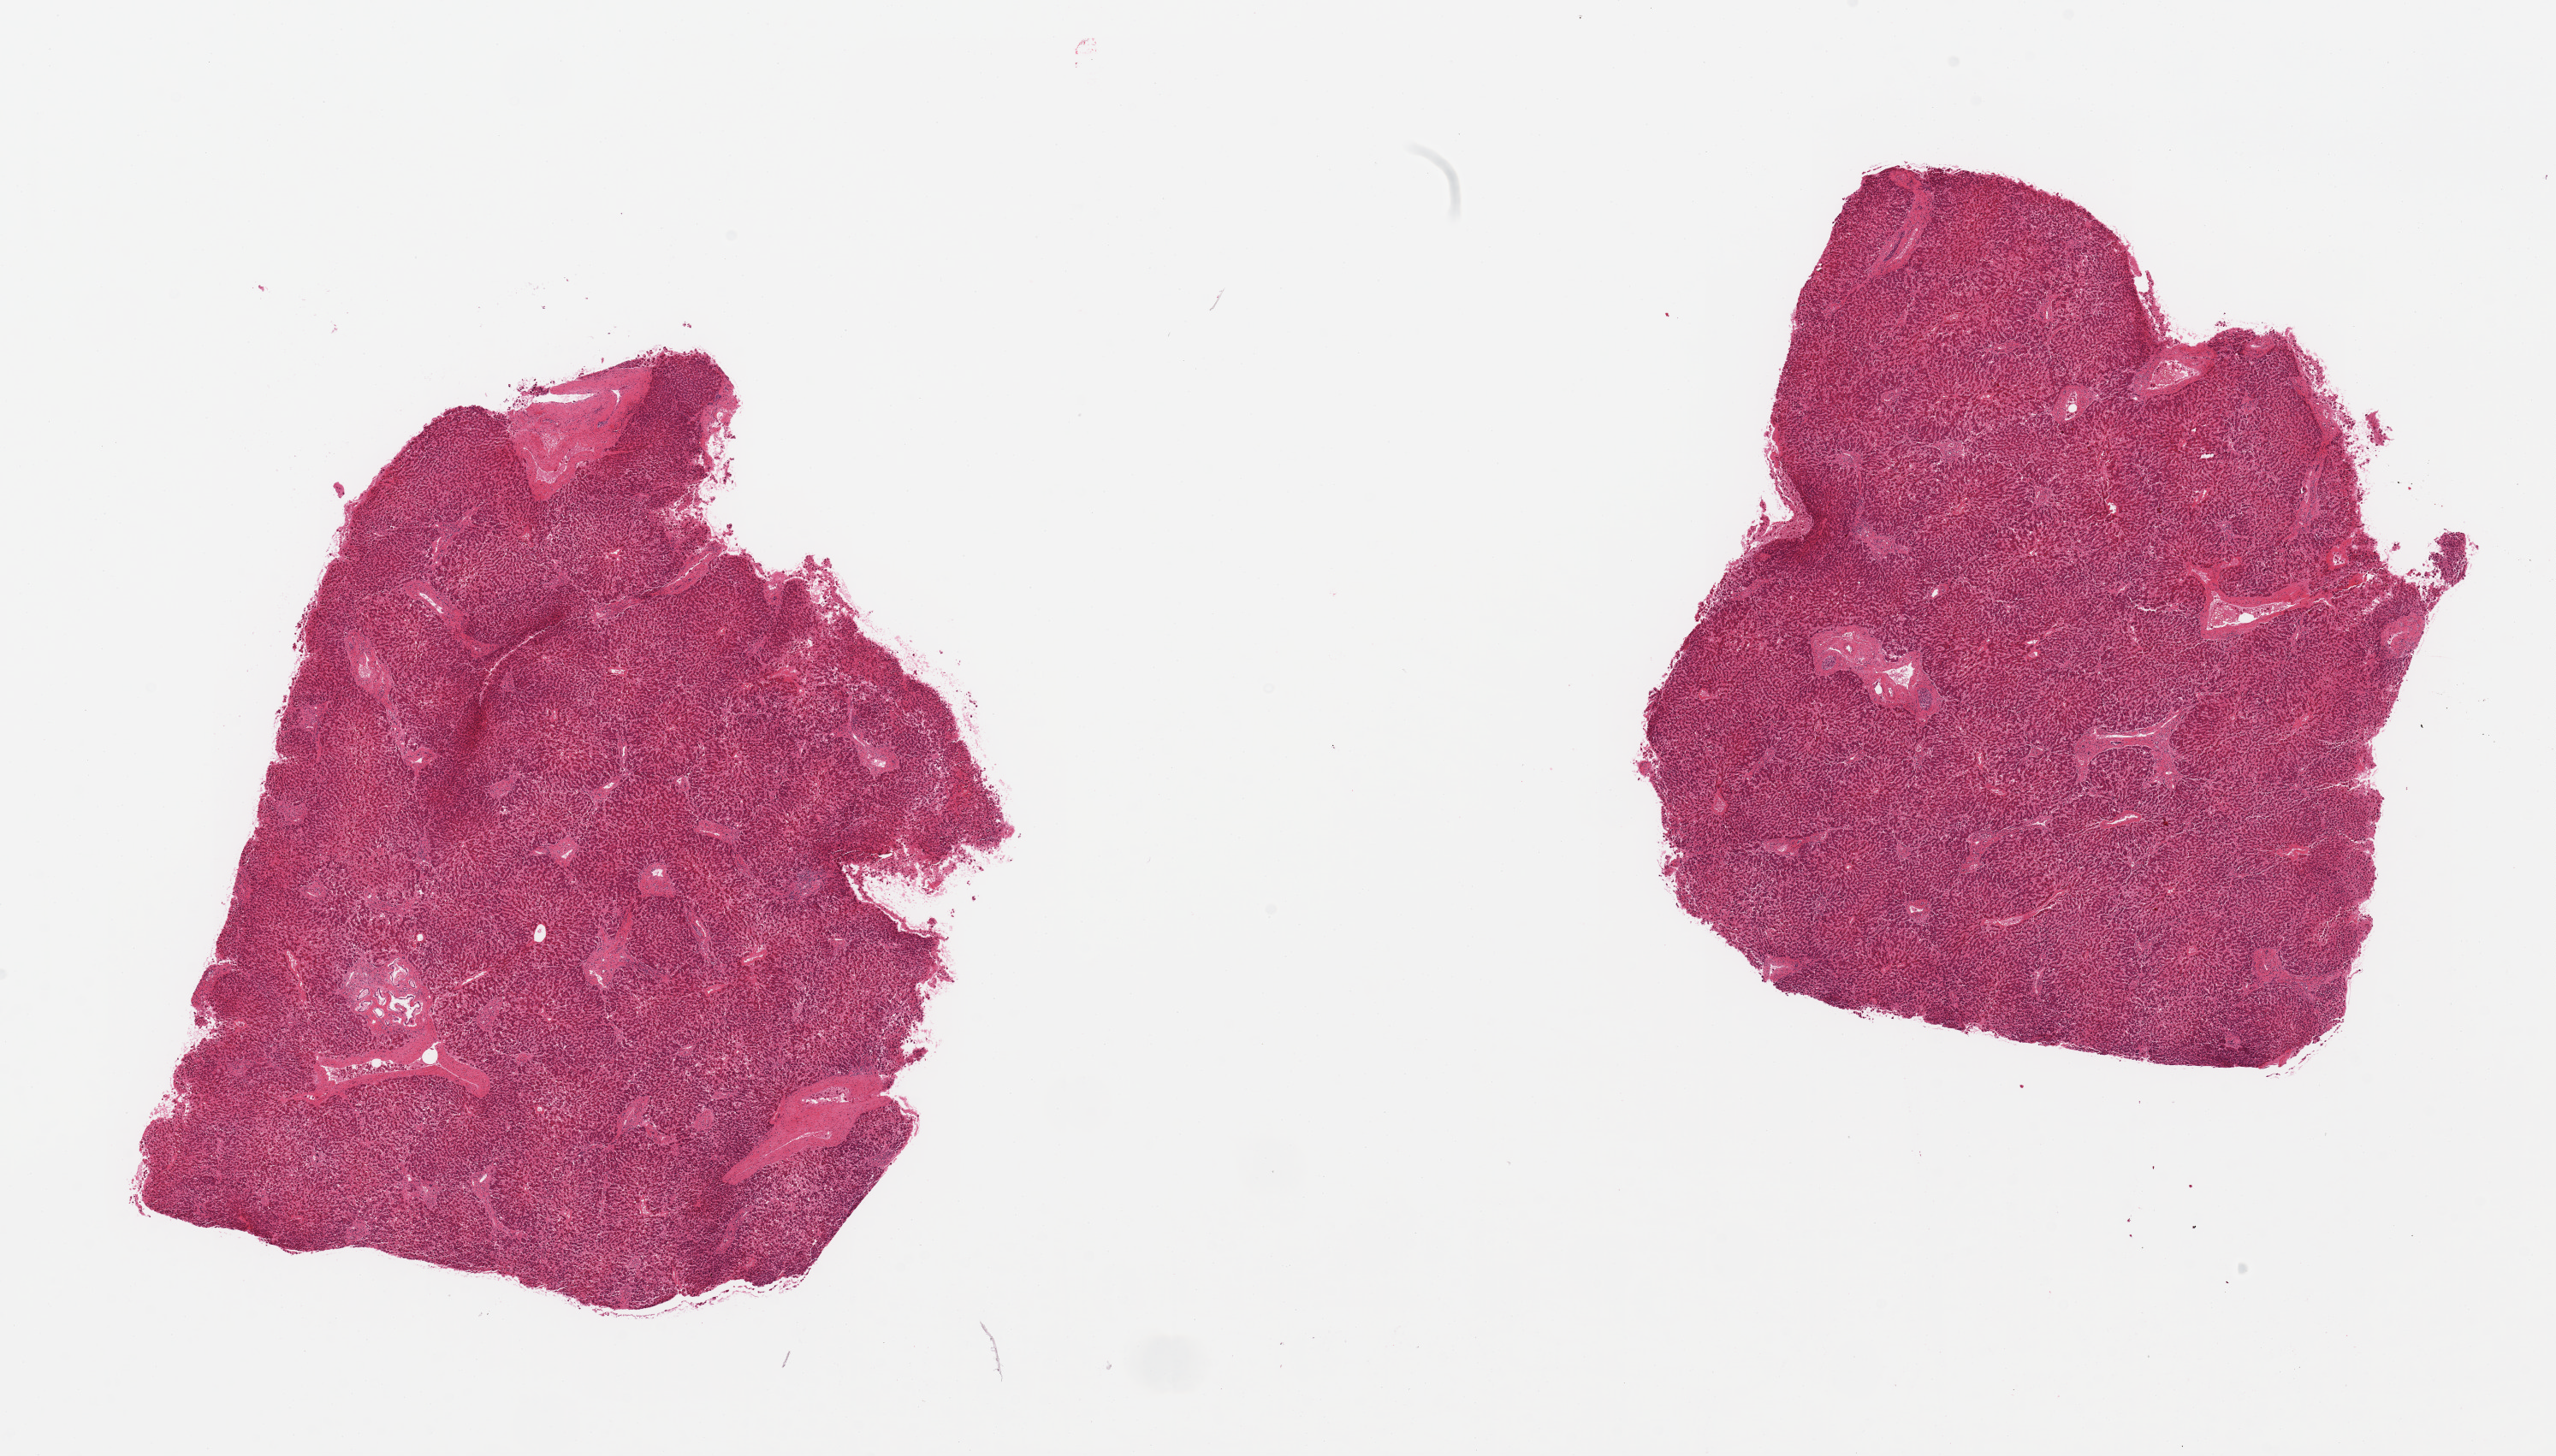
Digitized haematoxylin and eosin-stained section — low-resolution overview of the scanned area, about 23.6 x 13.5 mm; PAXgene-fixed paraffin-embedded (PFPE) section; sampled site (target tissue): liver; tissue donor sample.
• pathologist's review note for this sample: 2 pieces; moderate increase in periportal fibrous tissue, but little bridging and no nodules